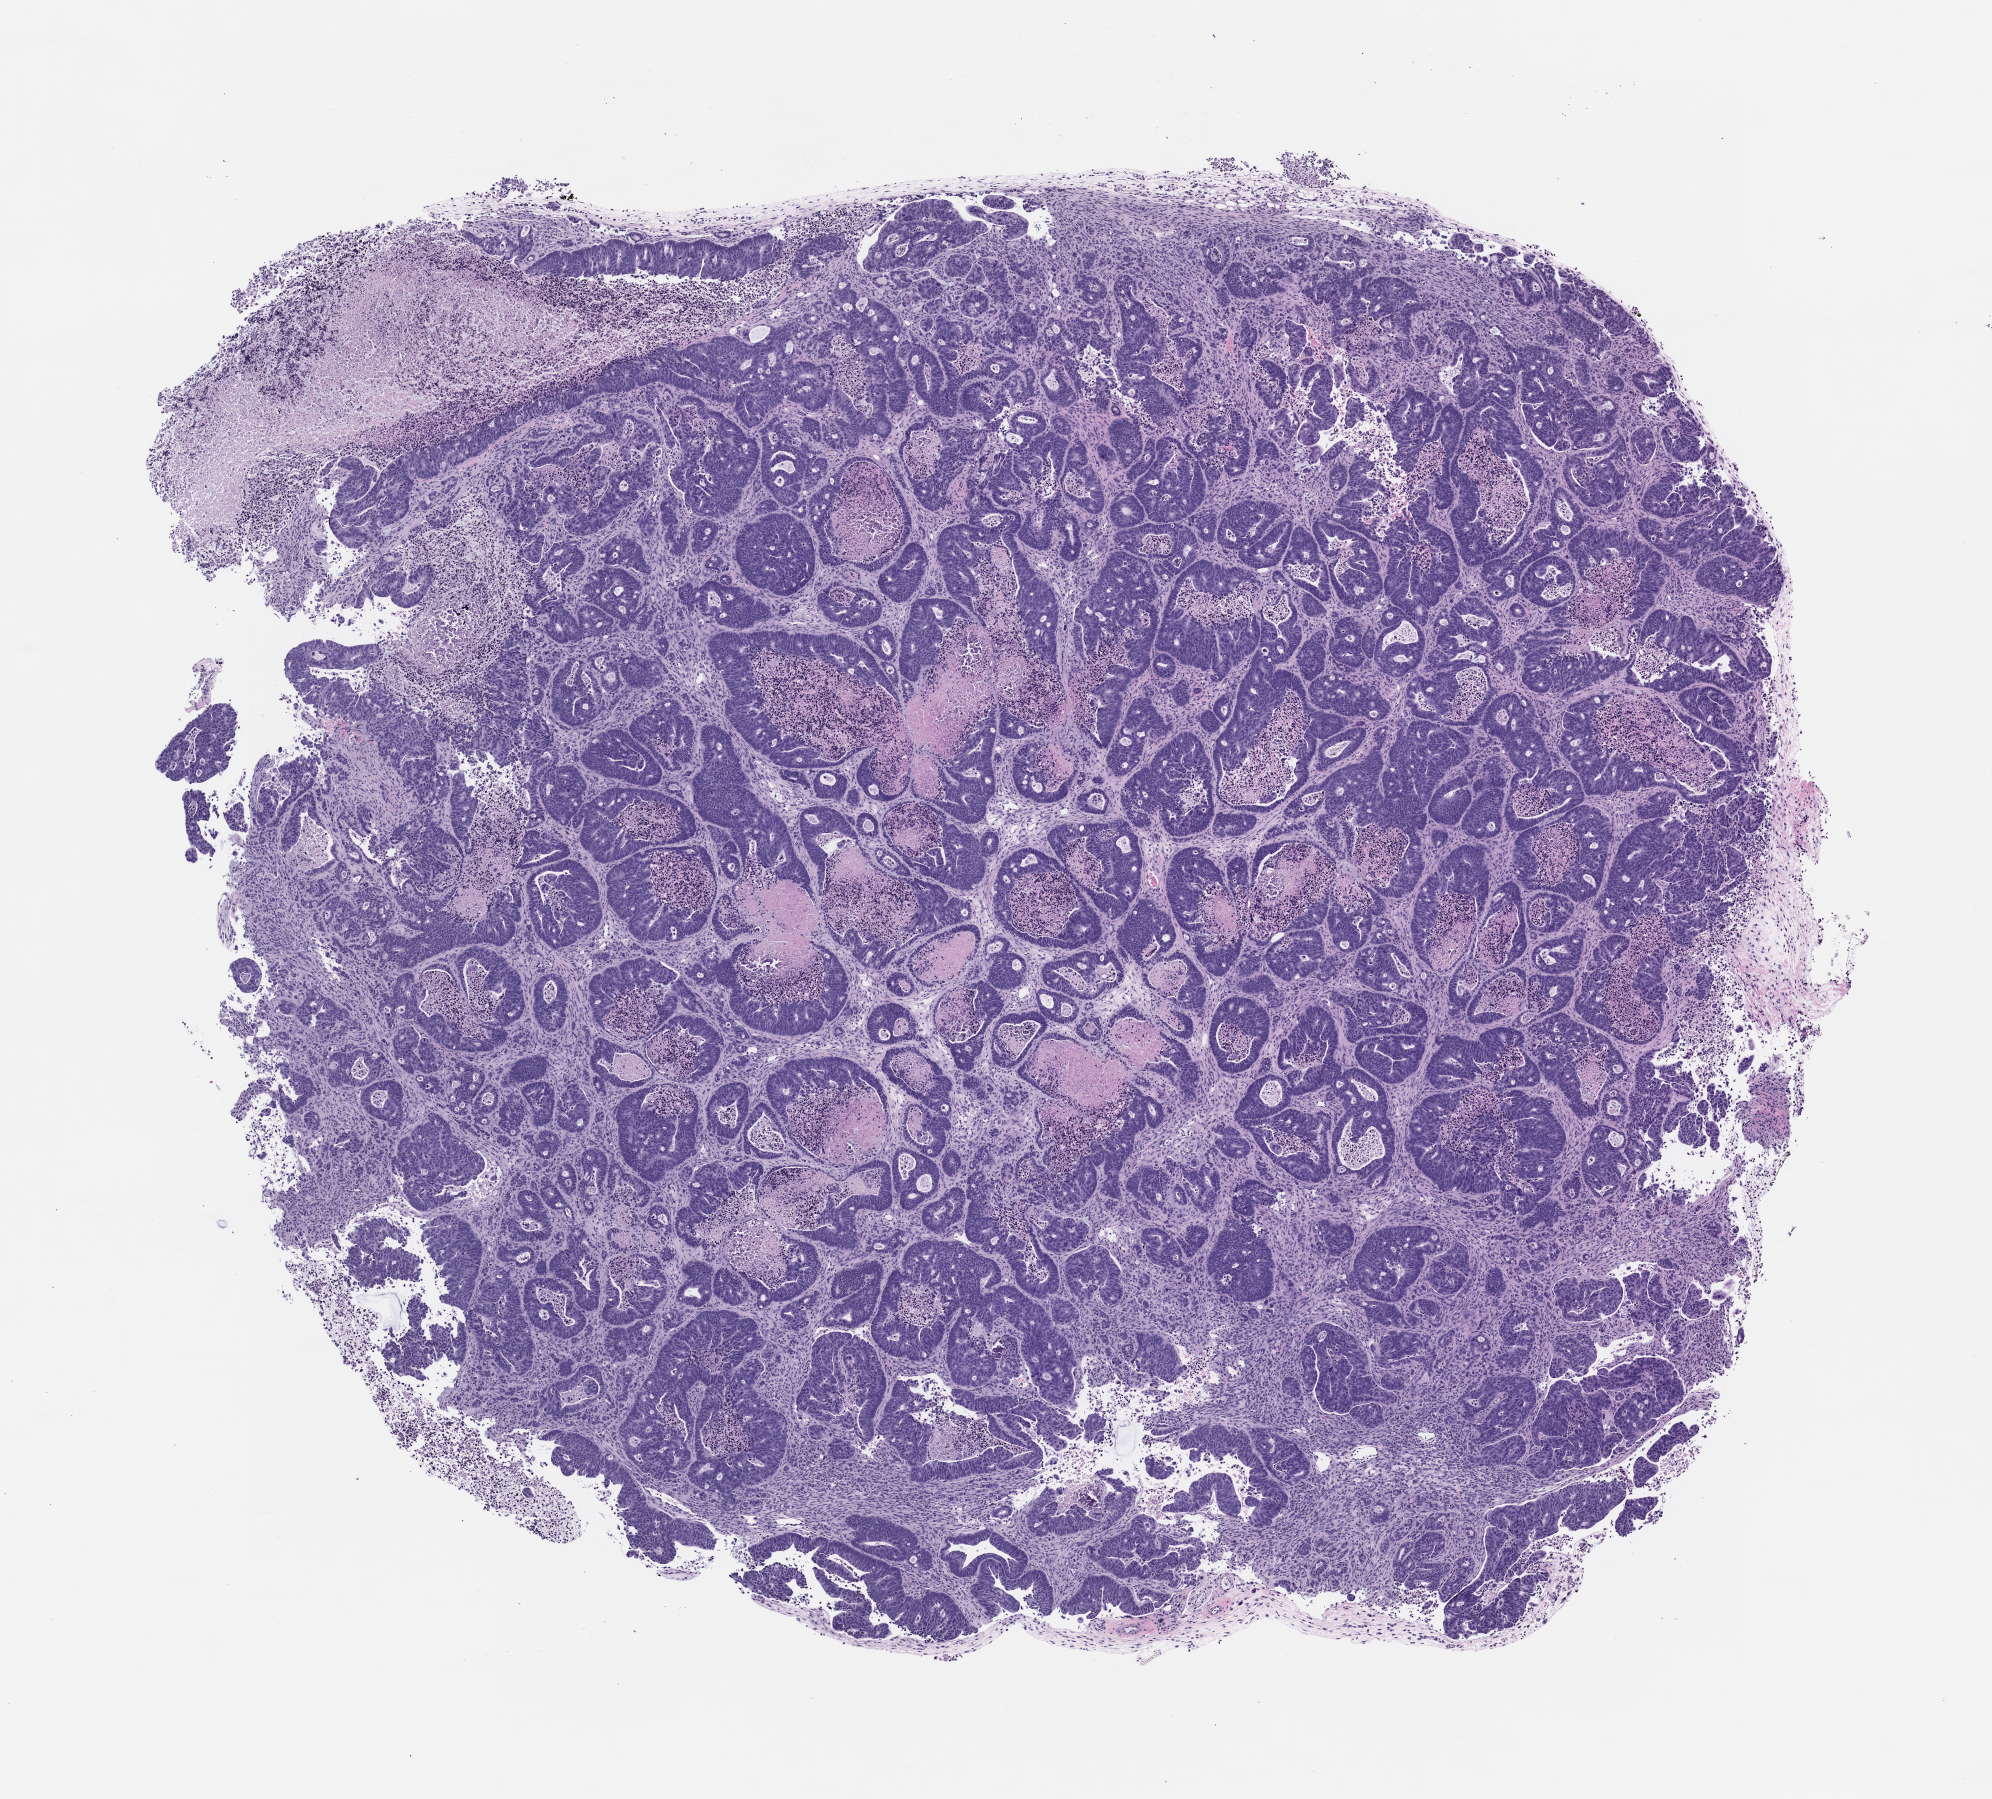
Haematoxylin and eosin whole-slide image of a patient-derived xenograft (PDX) tumor grown in a mouse, passage 1 — a low-resolution overview of the entire scanned area, about 8.0 x 7.2 mm, FFPE section, tumor site category: colon.
- originating patient diagnosis: Colon Adenocarcinoma